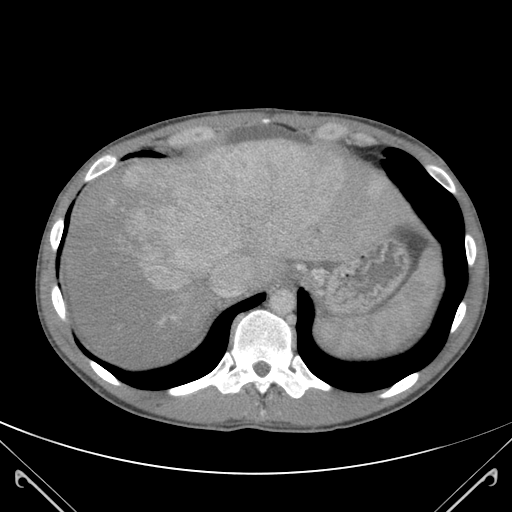
Contrast-enhanced abdominal CT (liver protocol), one axial slice; soft-tissue window (W 400 / L 40 HU); 3 mm slice thickness; 512 × 512 image matrix, field of view 380 × 380 mm. From the clinical record (not read from this slice): diagnosis: hepatocellular carcinoma (patient treated with transarterial chemoembolisation; whether this scan precedes or follows treatment is not stated here); TNM stage (as recorded): Stage-IIIB; Child-Pugh class: A.
Annotated regions visible in this slice (semi-automatically segmented with operator editing):
- abdominal aorta: box from (x=273, y=289) to (x=295, y=312) px
- liver parenchyma outside the tumour (the mass and vessels are separate outlines, so this box may not span the whole liver): (x=68, y=143)–(x=365, y=363)
- mass: (x=96, y=141)–(x=345, y=299)
- liver vessels: (x=209, y=155)–(x=338, y=297)